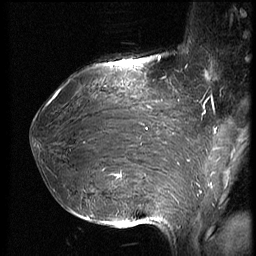
Breast MRI (dynamic contrast-enhanced), one sagittal slice; slice 27 of 66 in the series (ordered by position); dynamic contrast-enhanced series, image 2 of 3 at this slice position (ordered by acquisition); 1.5 T; TE 4.2 ms, TR 8.9 ms; 2.5 mm slice thickness; 256 × 256 image matrix, field of view 200 × 200 mm. Female patient, age 39 years. From the clinical record (not read from this slice): setting: breast cancer imaged before/during neoadjuvant chemotherapy; receptor status: HER2-positive.
Structures marked on this image (semi-automatic segmentation, software-assisted and operator-edited):
- analysis volume of interest (the breast-tissue region the enhancement analysis was run in; not a lesion): bounding box <32,75,188,218> (left, top, right, bottom; pixels)
- tumour enhancement mask (voxels above the 140 % enhancement threshold inside the analysis volume of interest): <53,91,147,211>